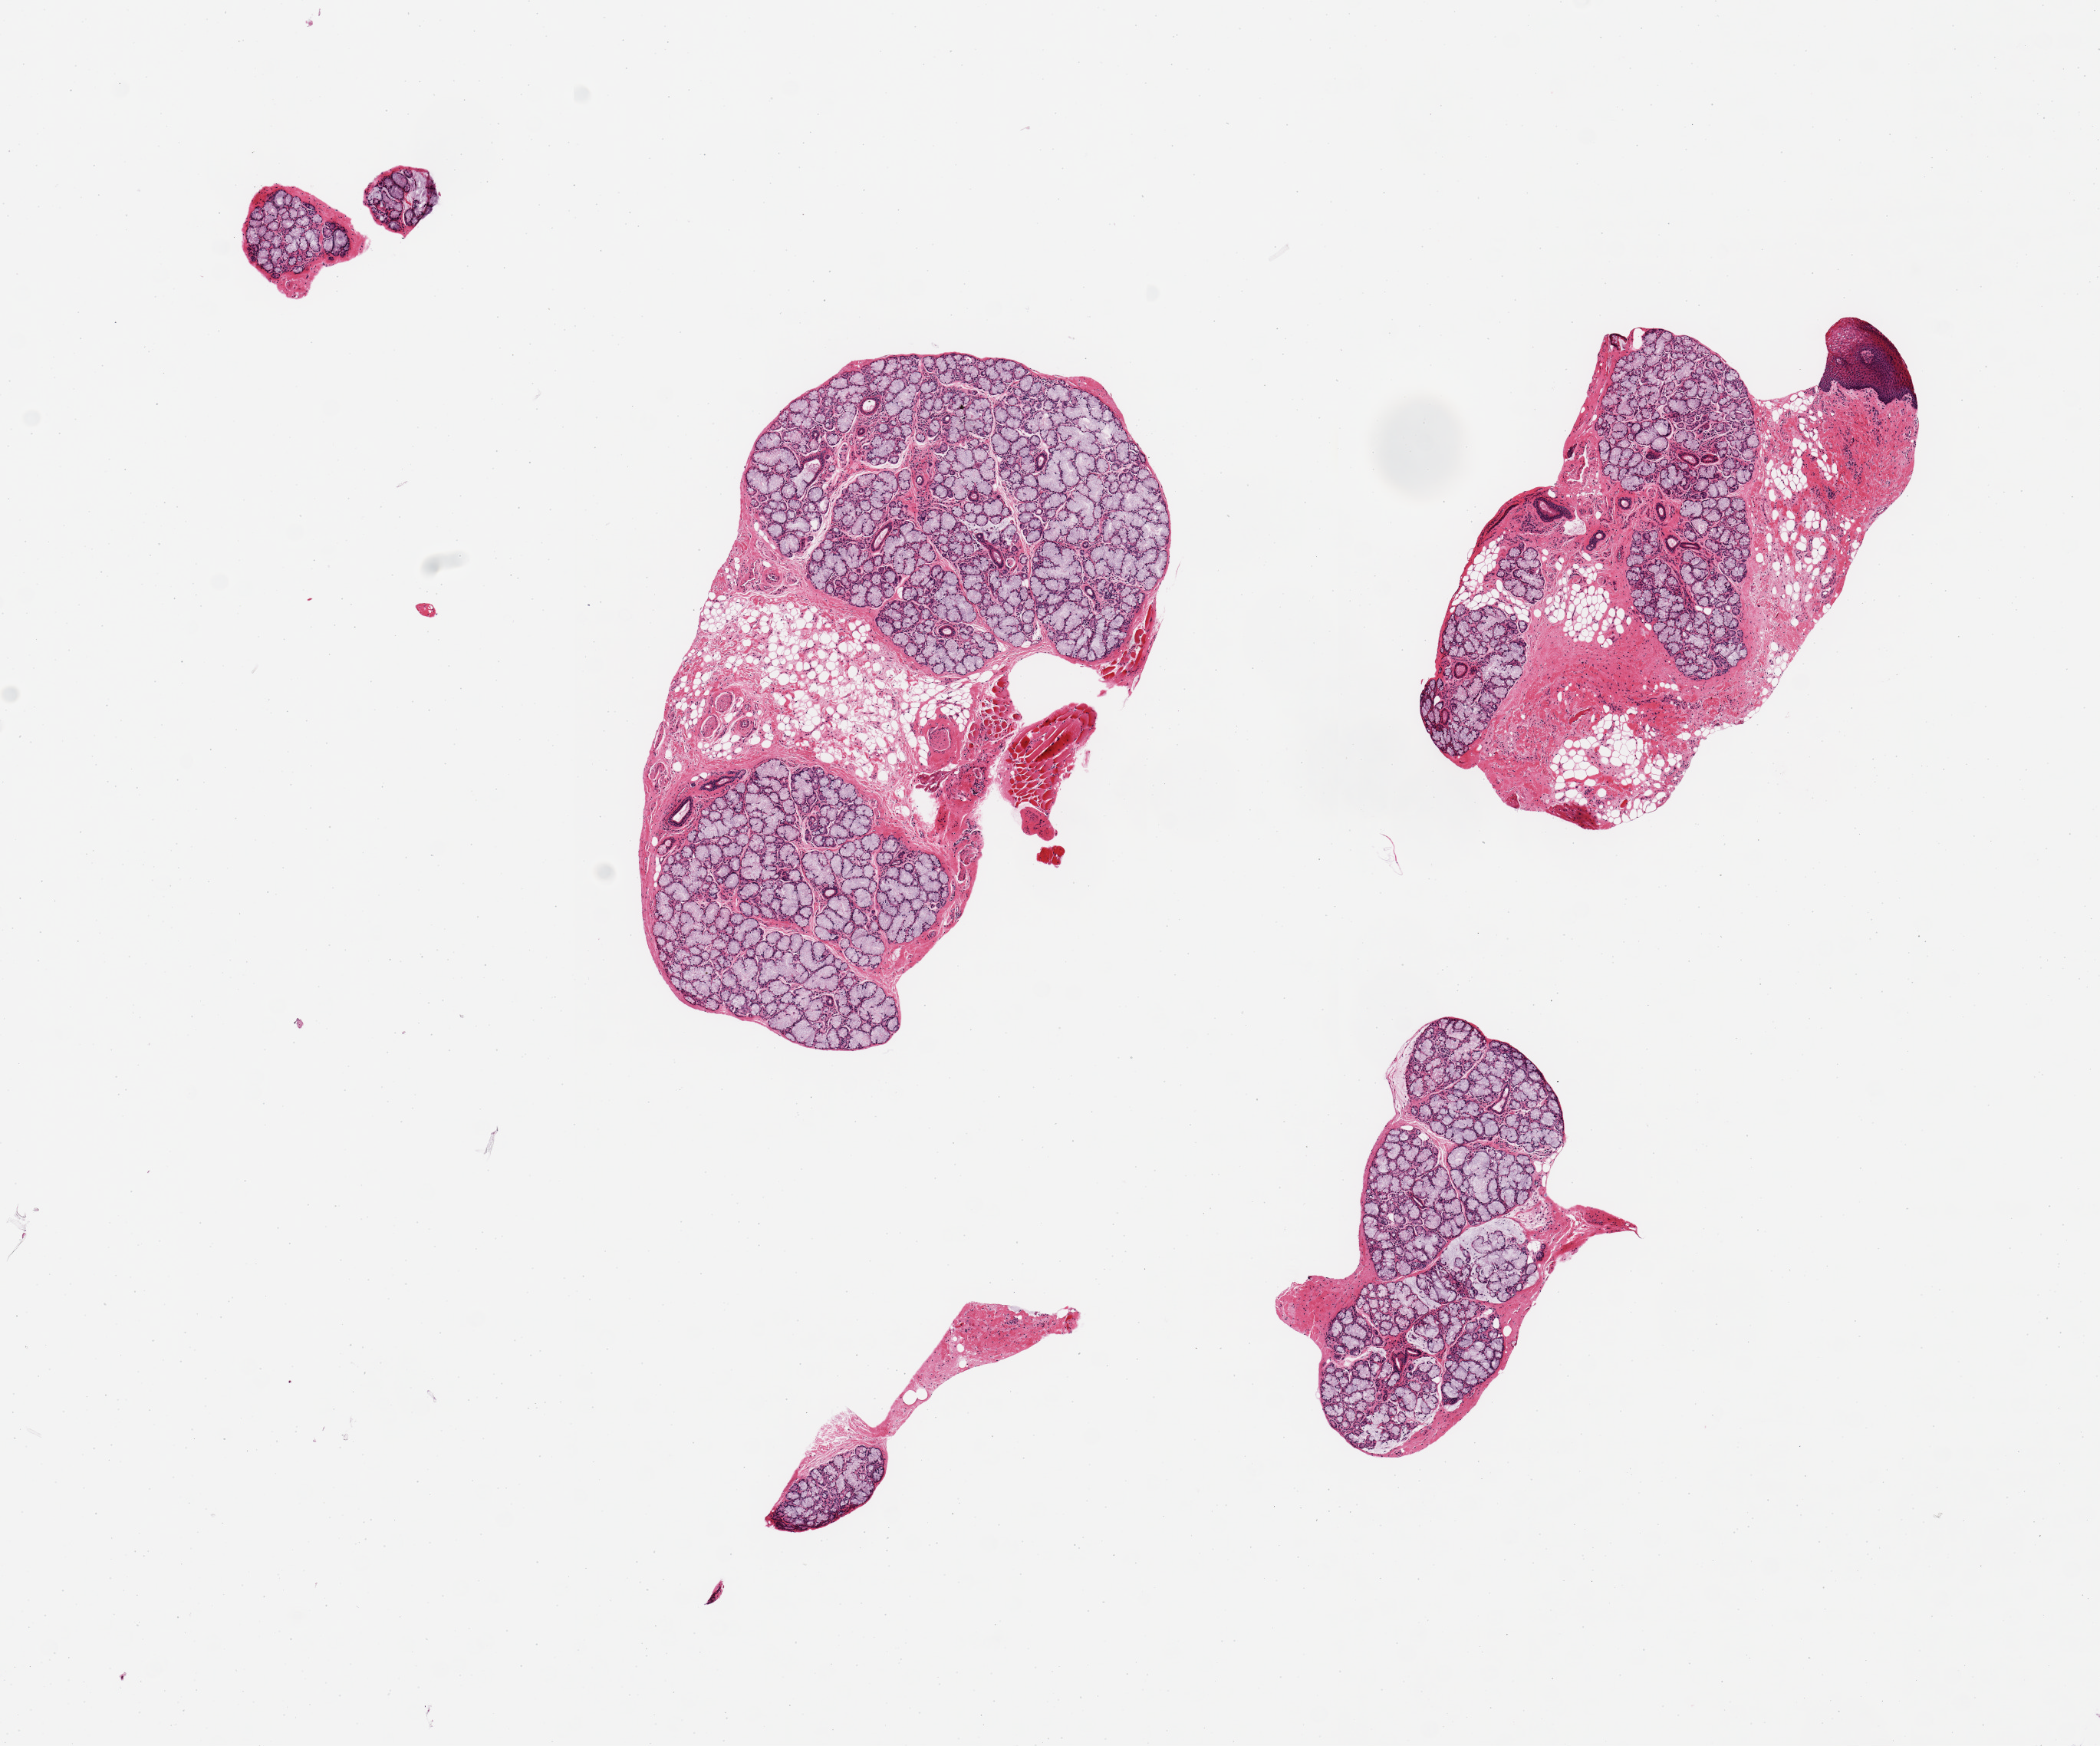
Digitized H&E-stained section, shown as a low-resolution overview of the whole scanned area (about 10.8 x 9.0 mm); PAXgene-fixed, paraffin-embedded tissue; section of minor salivary gland (target tissue); tissue donor sample.
• review note (as recorded): 3 pieces (fragmented), target glandular elements ~70% of tissue; rest is stroma